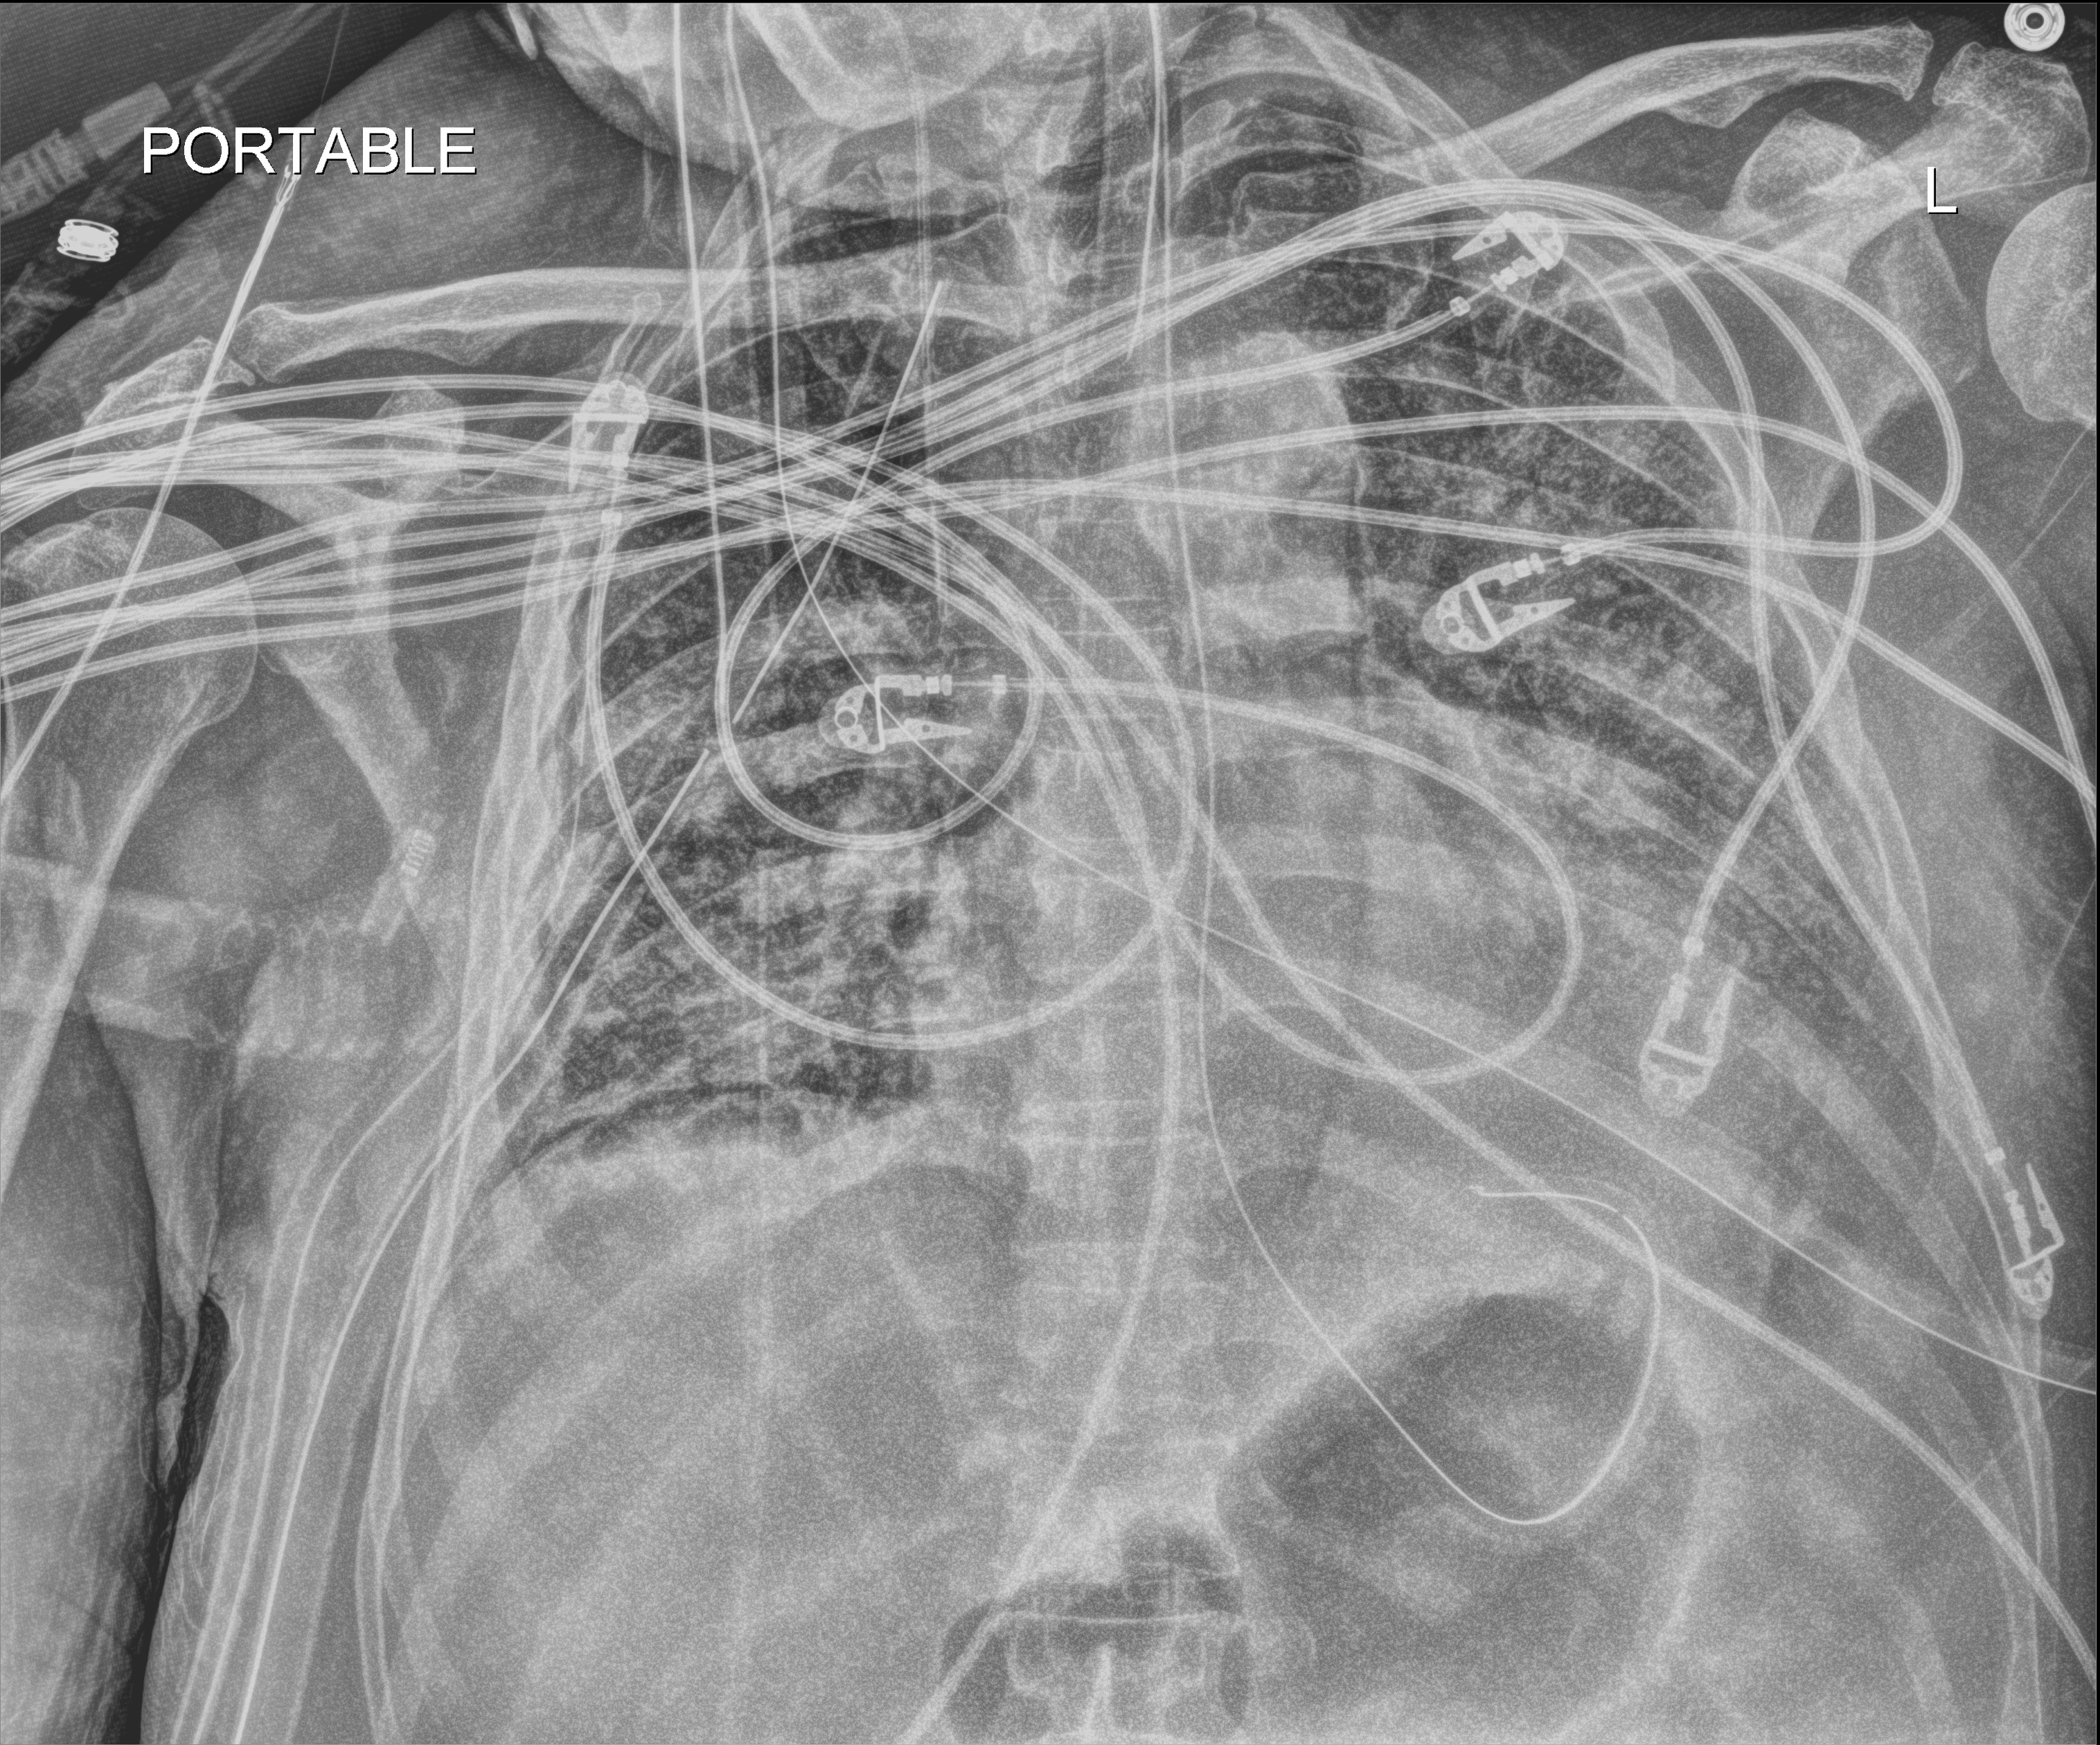
Portable chest radiograph; anteroposterior (AP) projection. Patient hospitalised with COVID-19; male, aged 60–74 years.
Admission-level facts for this patient (not findings on this image; timing relative to this image not recorded):
- admitted to intensive care during this hospital stay: yes
- mechanically ventilated during this hospital stay: yes